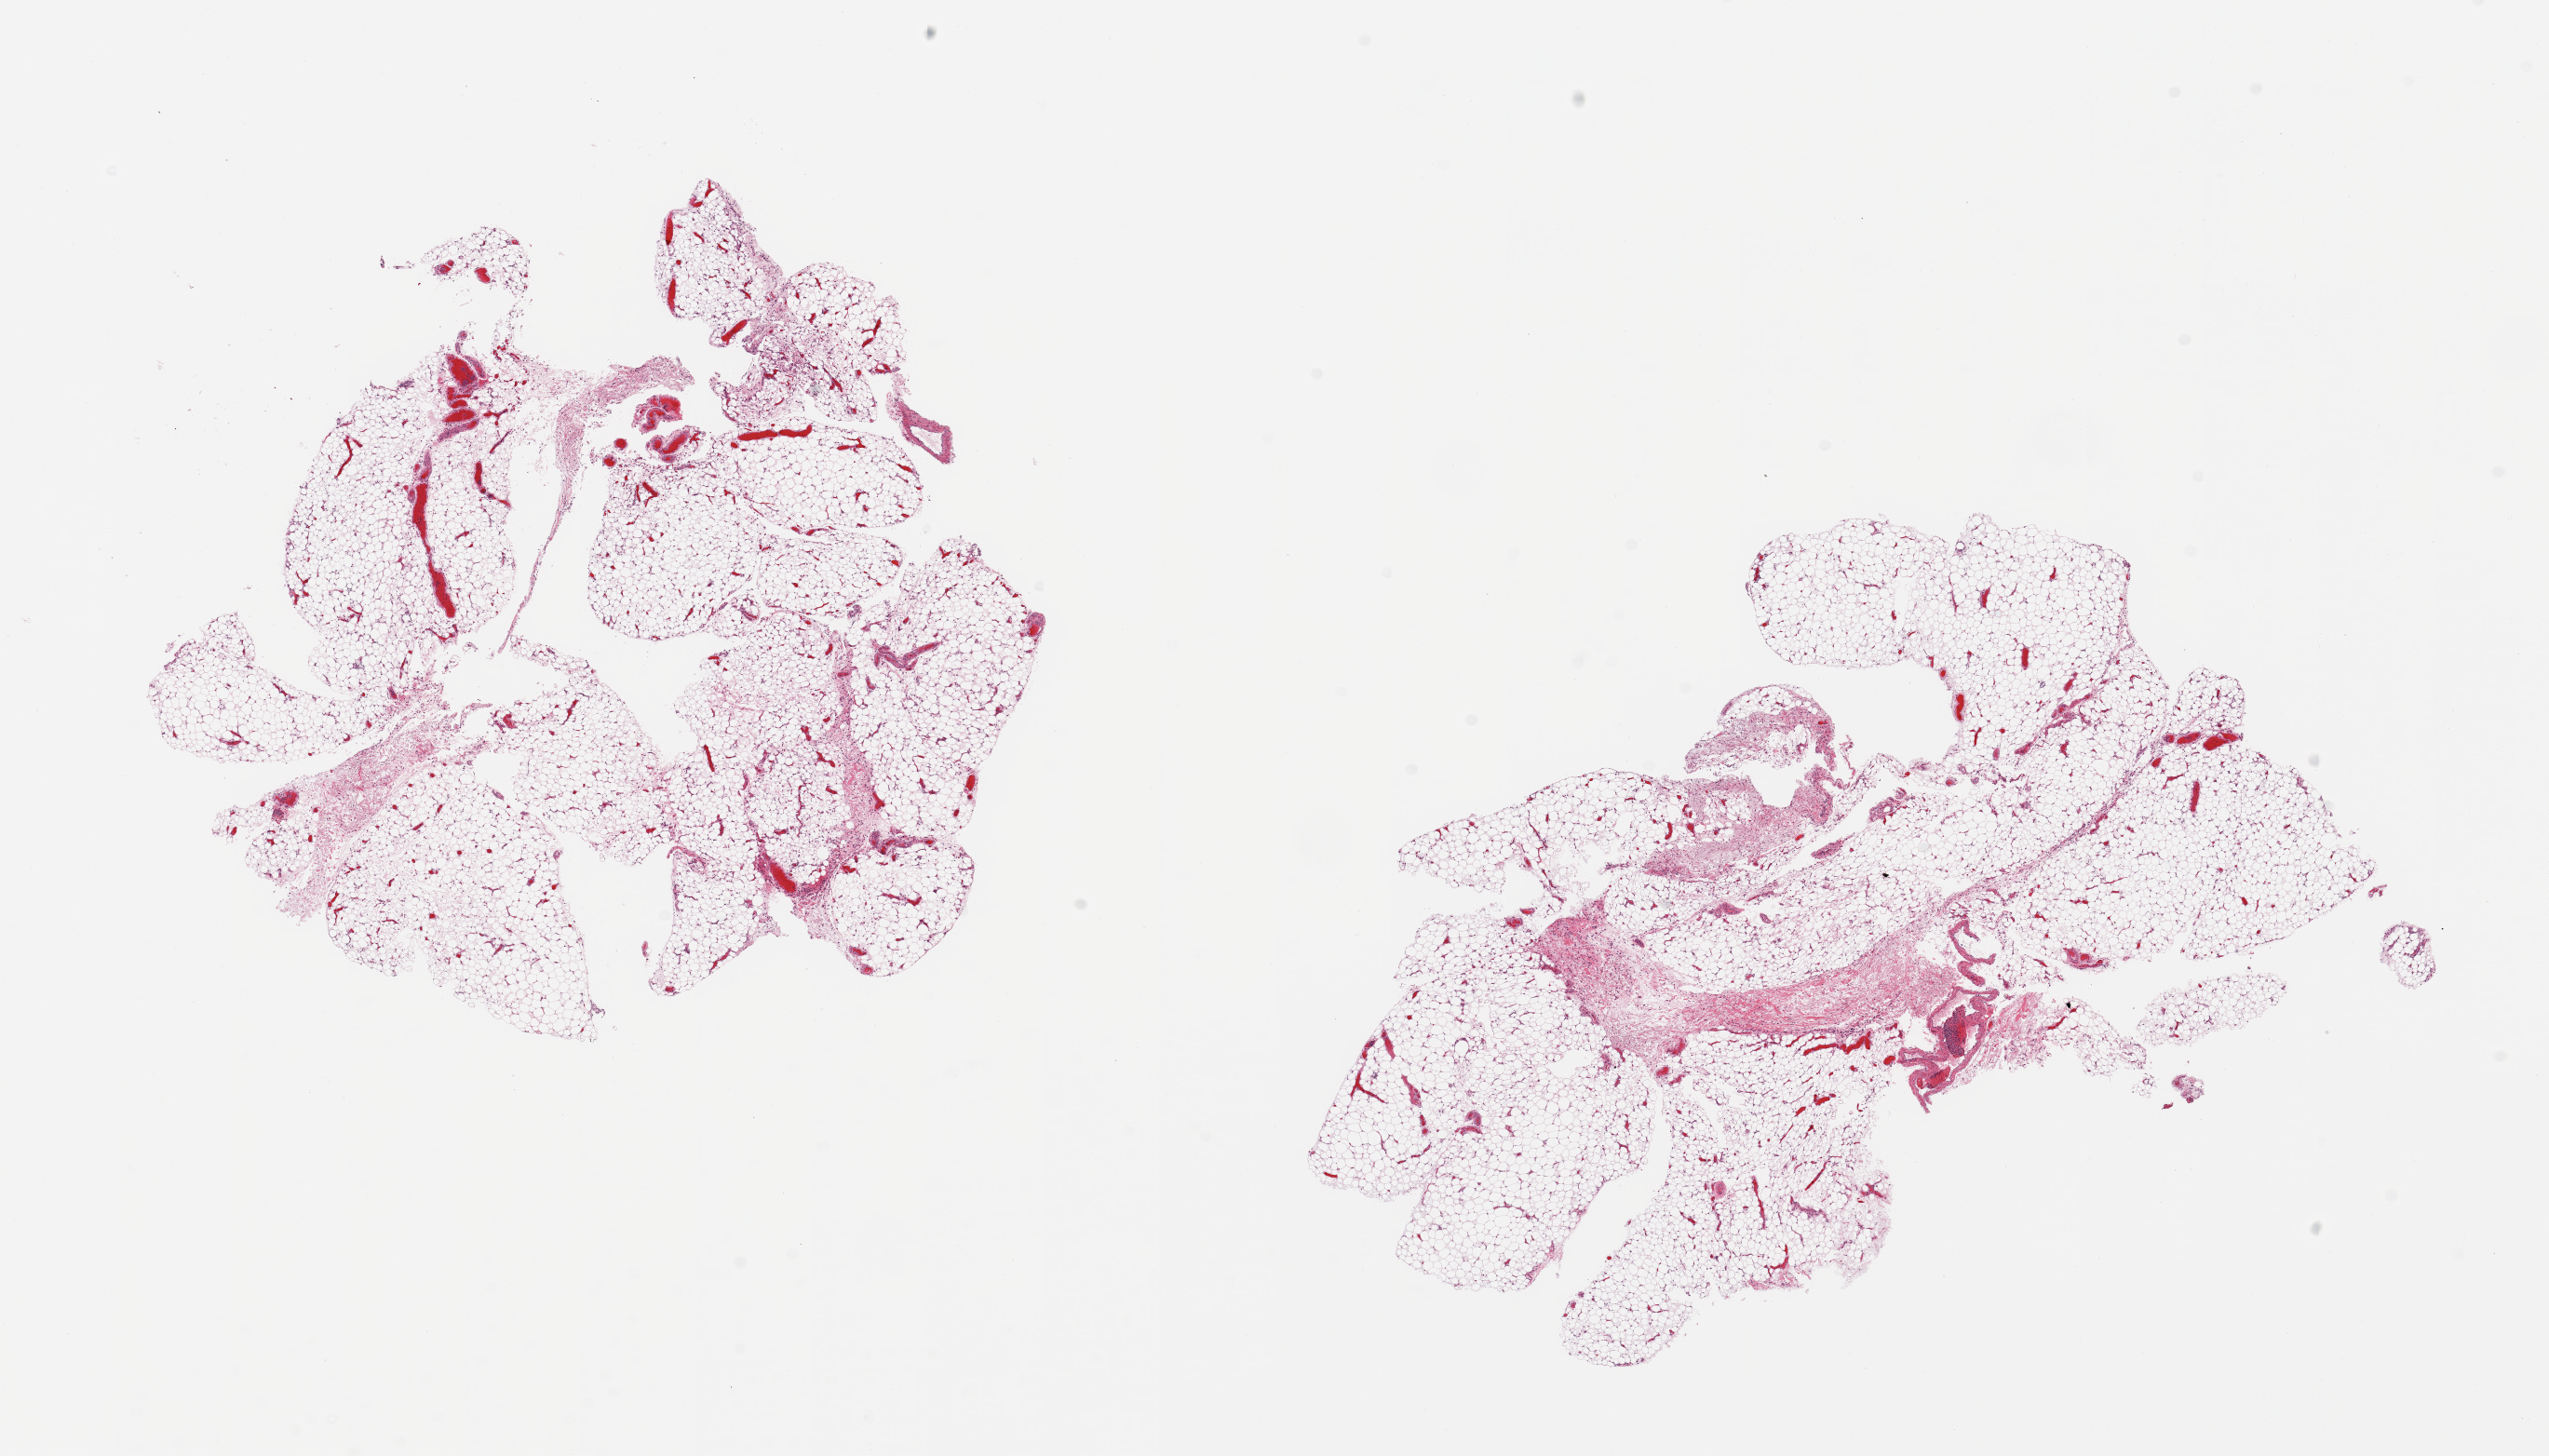
Whole-slide image, H&E stain, a low-resolution overview of the entire scanned area, about 21.7 x 12.4 mm. PAXgene-fixed, paraffin-embedded tissue. Section of adipose tissue (target tissue). Tissue donor sample. Donor sex: female.
Pathologist's review note for this sample: 2 pieces, ~10% fascia.